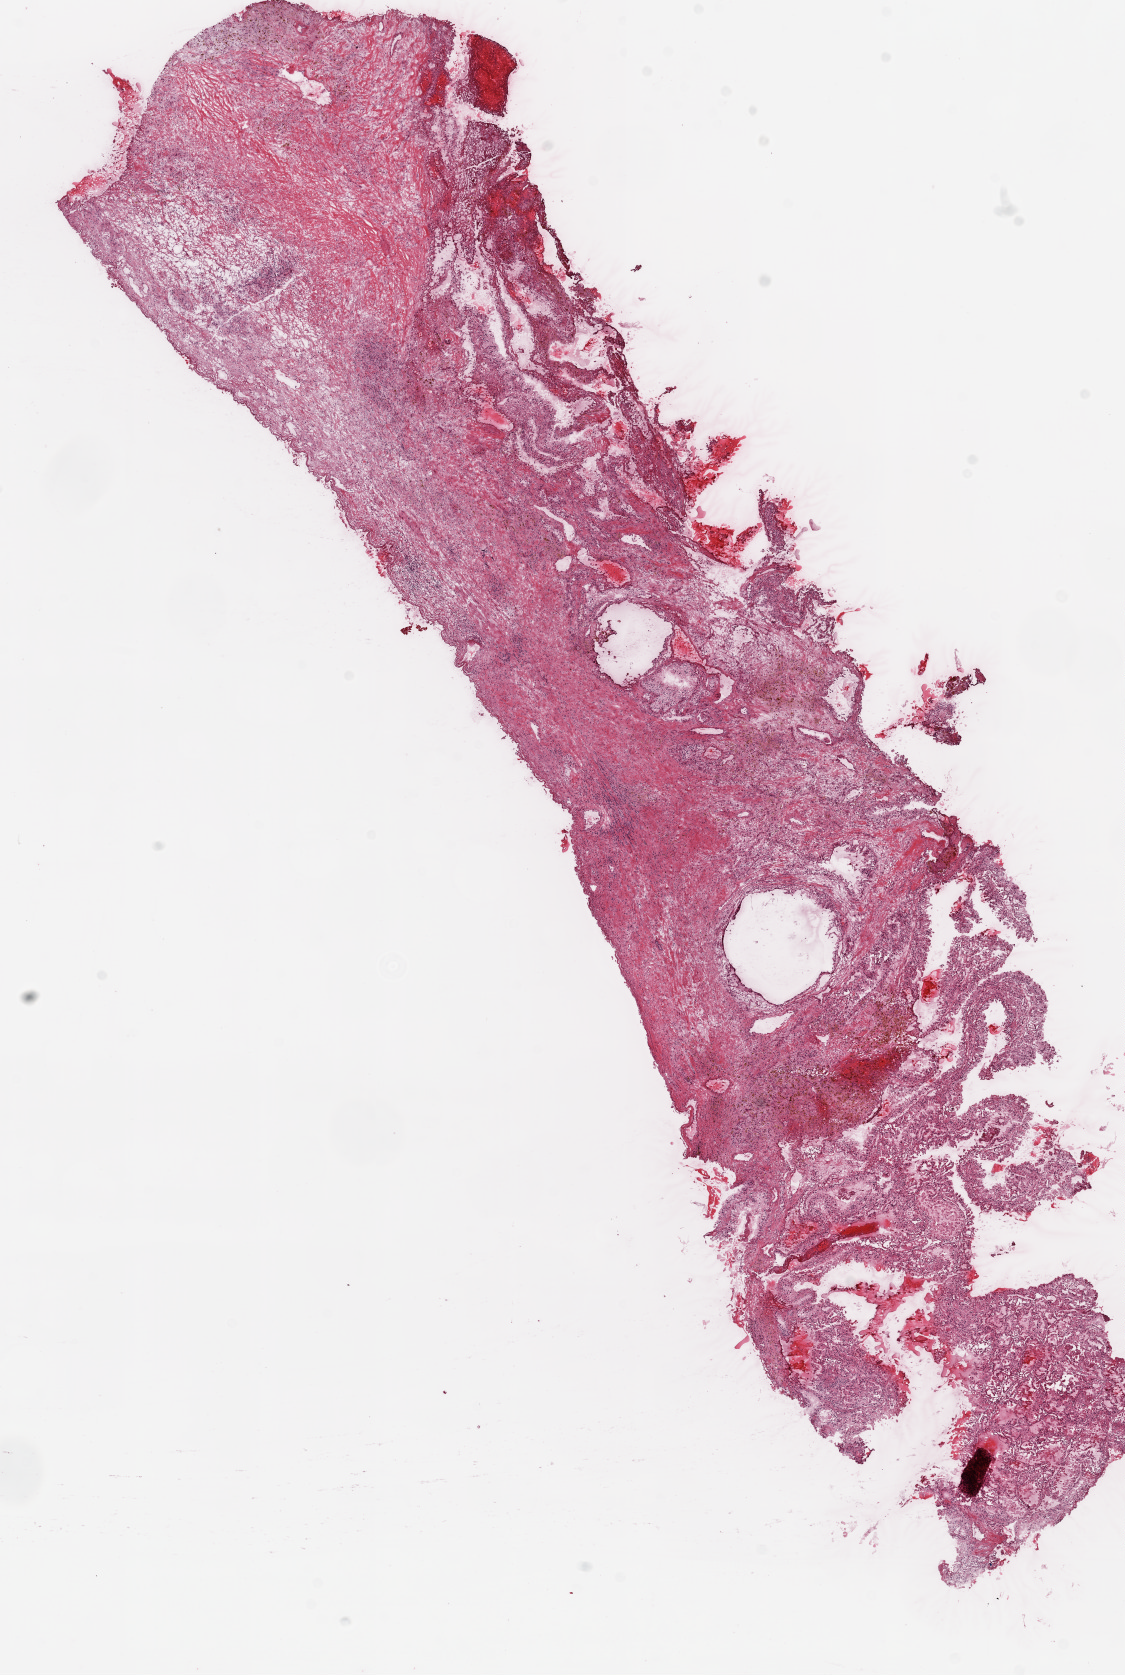
Digitized H&E tissue section (whole slide) — low-resolution overview of the scanned area, about 9.0 x 13.4 mm (acquisition: 20x scan); frozen section; kidney, primary tumour sample. Male, age 56 years at initial diagnosis. Histologic grade: G3 (poorly differentiated). Slide review estimates, as recorded: tumour cells 40%, tumour nuclei 70%, normal cells 0%, stromal cells 60%, necrosis 0%.
AJCC pathologic stage: I. TNM: T1a N0 M0. Histologic diagnosis: Clear cell adenocarcinoma, NOS. Lymph nodes positive (case pathology): 0 of 1 examined.